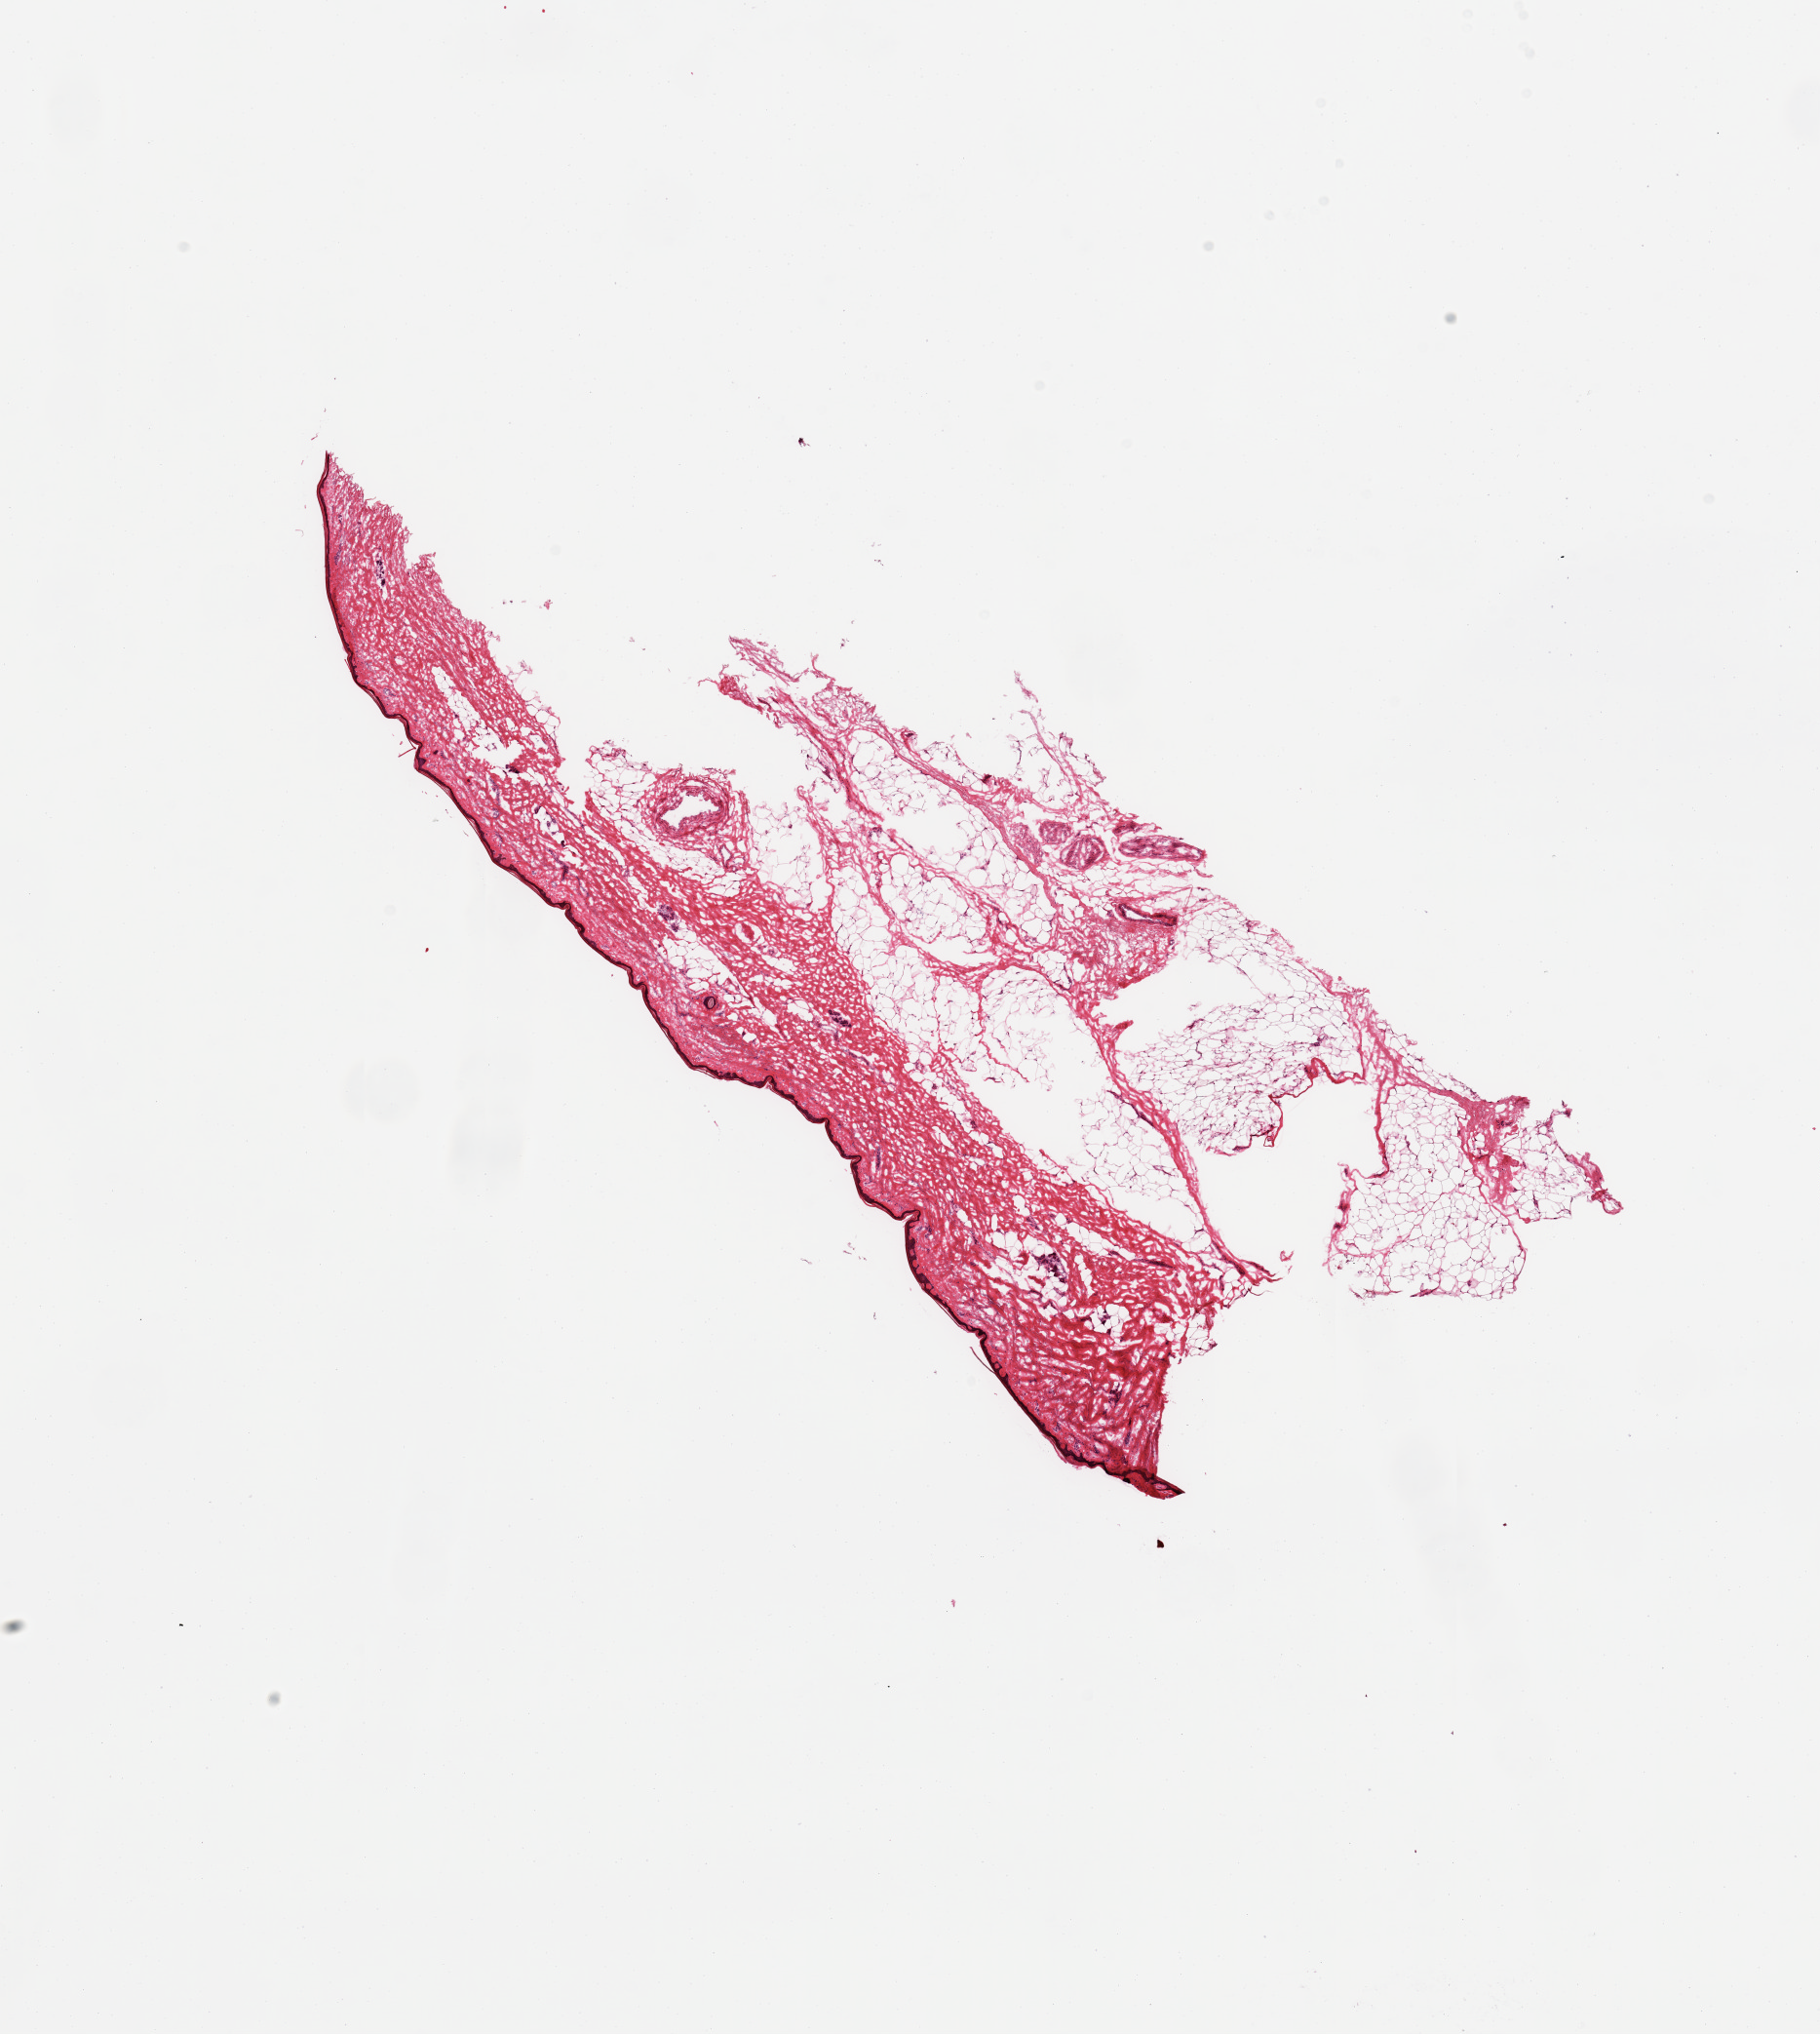
H&E whole-slide image — shown as a low-resolution overview of the whole scanned area (about 14.8 x 16.5 mm). Donor: female.
Specimen: frozen section (dry ice); section of skin of lower leg (target tissue); donor tissue sample.